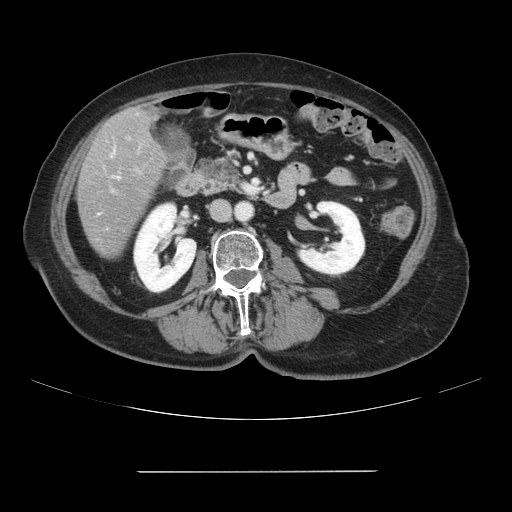
Contrast-enhanced abdominal CT, one axial slice. Slice 24 of 111 in the series (ordered by position). 120 kVp. Intravenous contrast given. Soft-tissue window (W 400 / L 40 HU). 2.5 mm slice thickness. 512 × 512 image matrix, field of view 400 × 400 mm. Female patient, age 74 years. From the clinical record (not read from this slice): diagnosis: colorectal cancer liver metastases, imaged before liver resection.
Outlined on this slice (outlined manually by an expert reader):
- liver: bounding box [x1, y1, x2, y2] px = [77, 107, 167, 259]